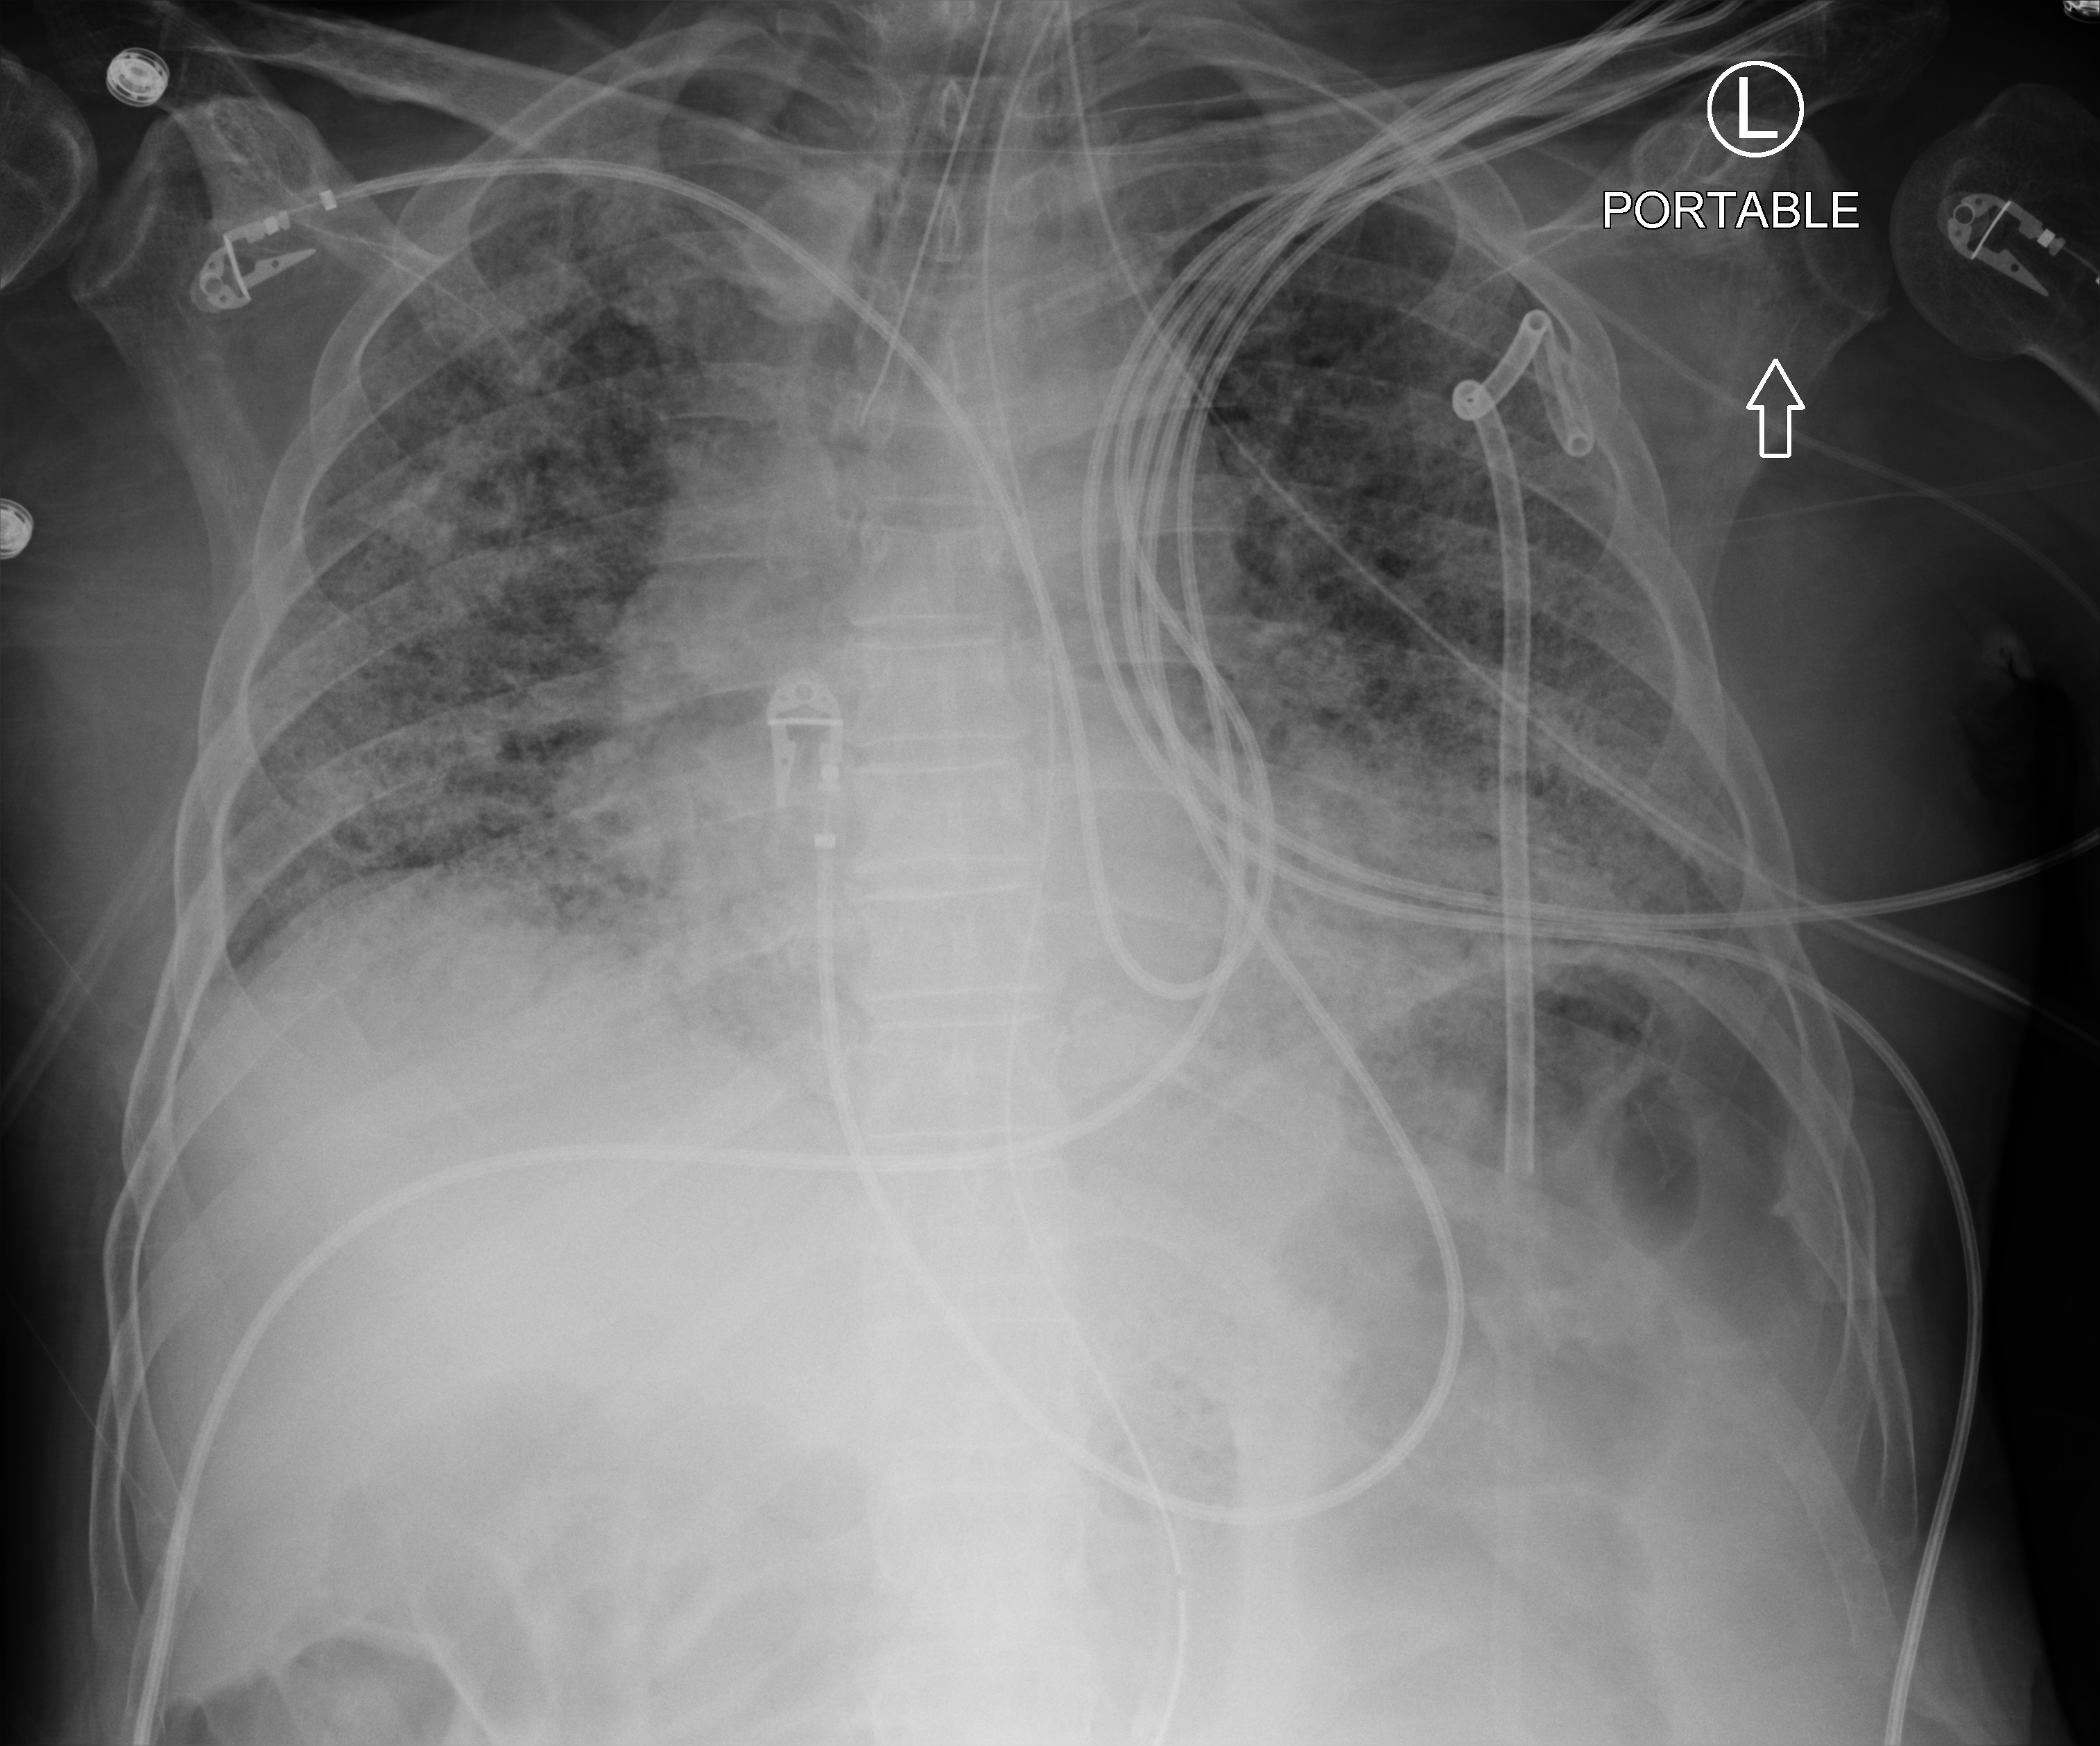
Chest X-ray (portable), anteroposterior (AP) projection. Patient hospitalised with COVID-19; male, aged 60–74 years.
Hospital-stay facts (about this admission, not read from this image; timing relative to this image not recorded): admitted to intensive care during this hospital stay: yes; mechanically ventilated during this hospital stay: yes.